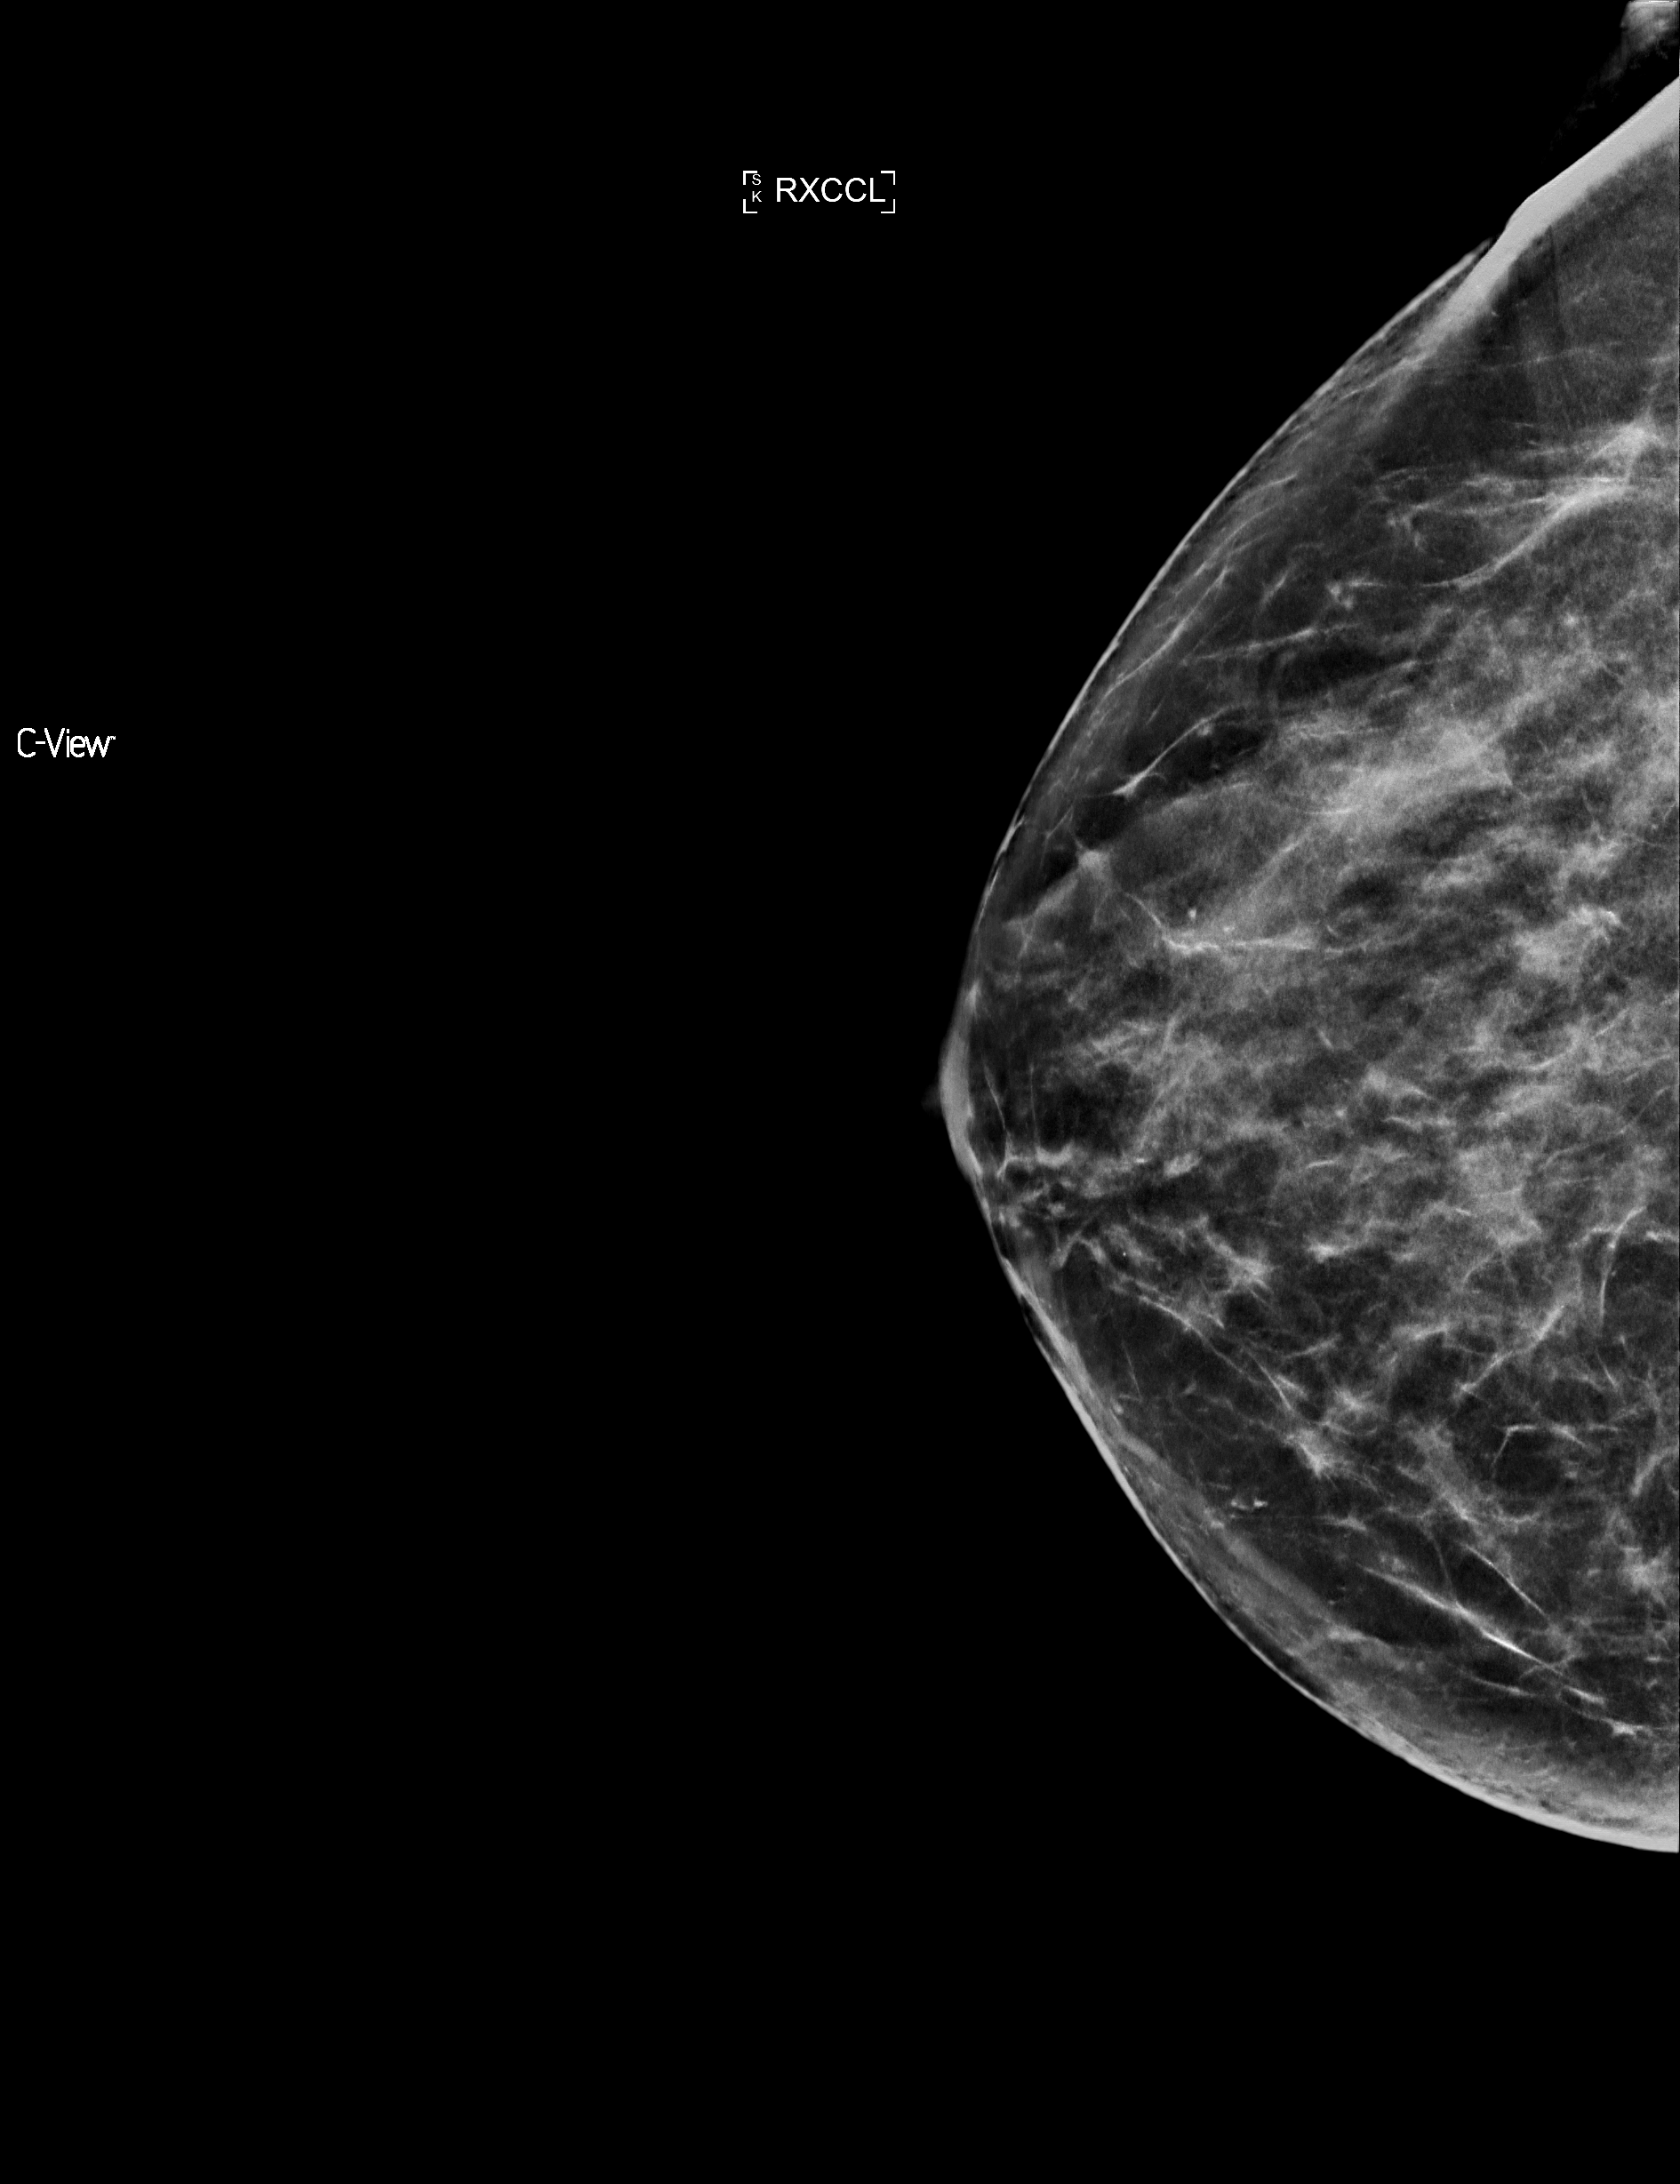
Full-field digital mammogram (FFDM), right breast, exaggerated CC view (lateral), screening examination, compressed breast thickness 56 mm. Patient aged 59 years (female).
BI-RADS breast density category at the screening exam (both breasts, scale 1–4): 3. Final BI-RADS assessment for this screening round (tomosynthesis exam, both breasts): category 1. Recall: no recall after this screen.